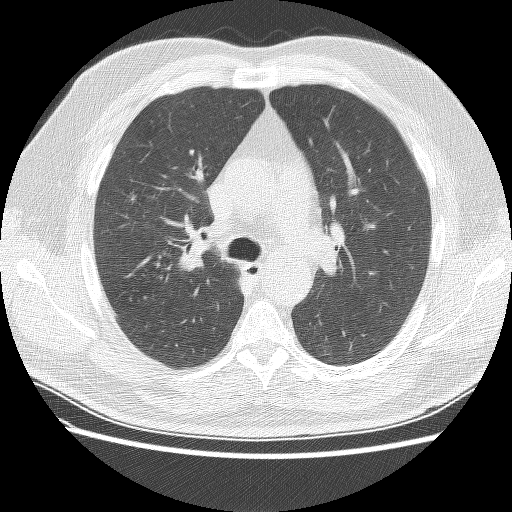
Chest CT (low-dose screening protocol), one axial image, baseline screening round, lung window (W 1500 / L -600 HU), 2.5 mm slice thickness, slice 63 of 159 in the series, 512 × 512 image matrix. Male, age 57 years at enrolment. Current smoker at enrolment.
Lesion marked by an expert reader, bounding box (x1, y1, x2, y2) in pixels: (159, 239, 213, 293). No non-calcified nodule or mass ≥4 mm was recorded by the screening reader at this exam.